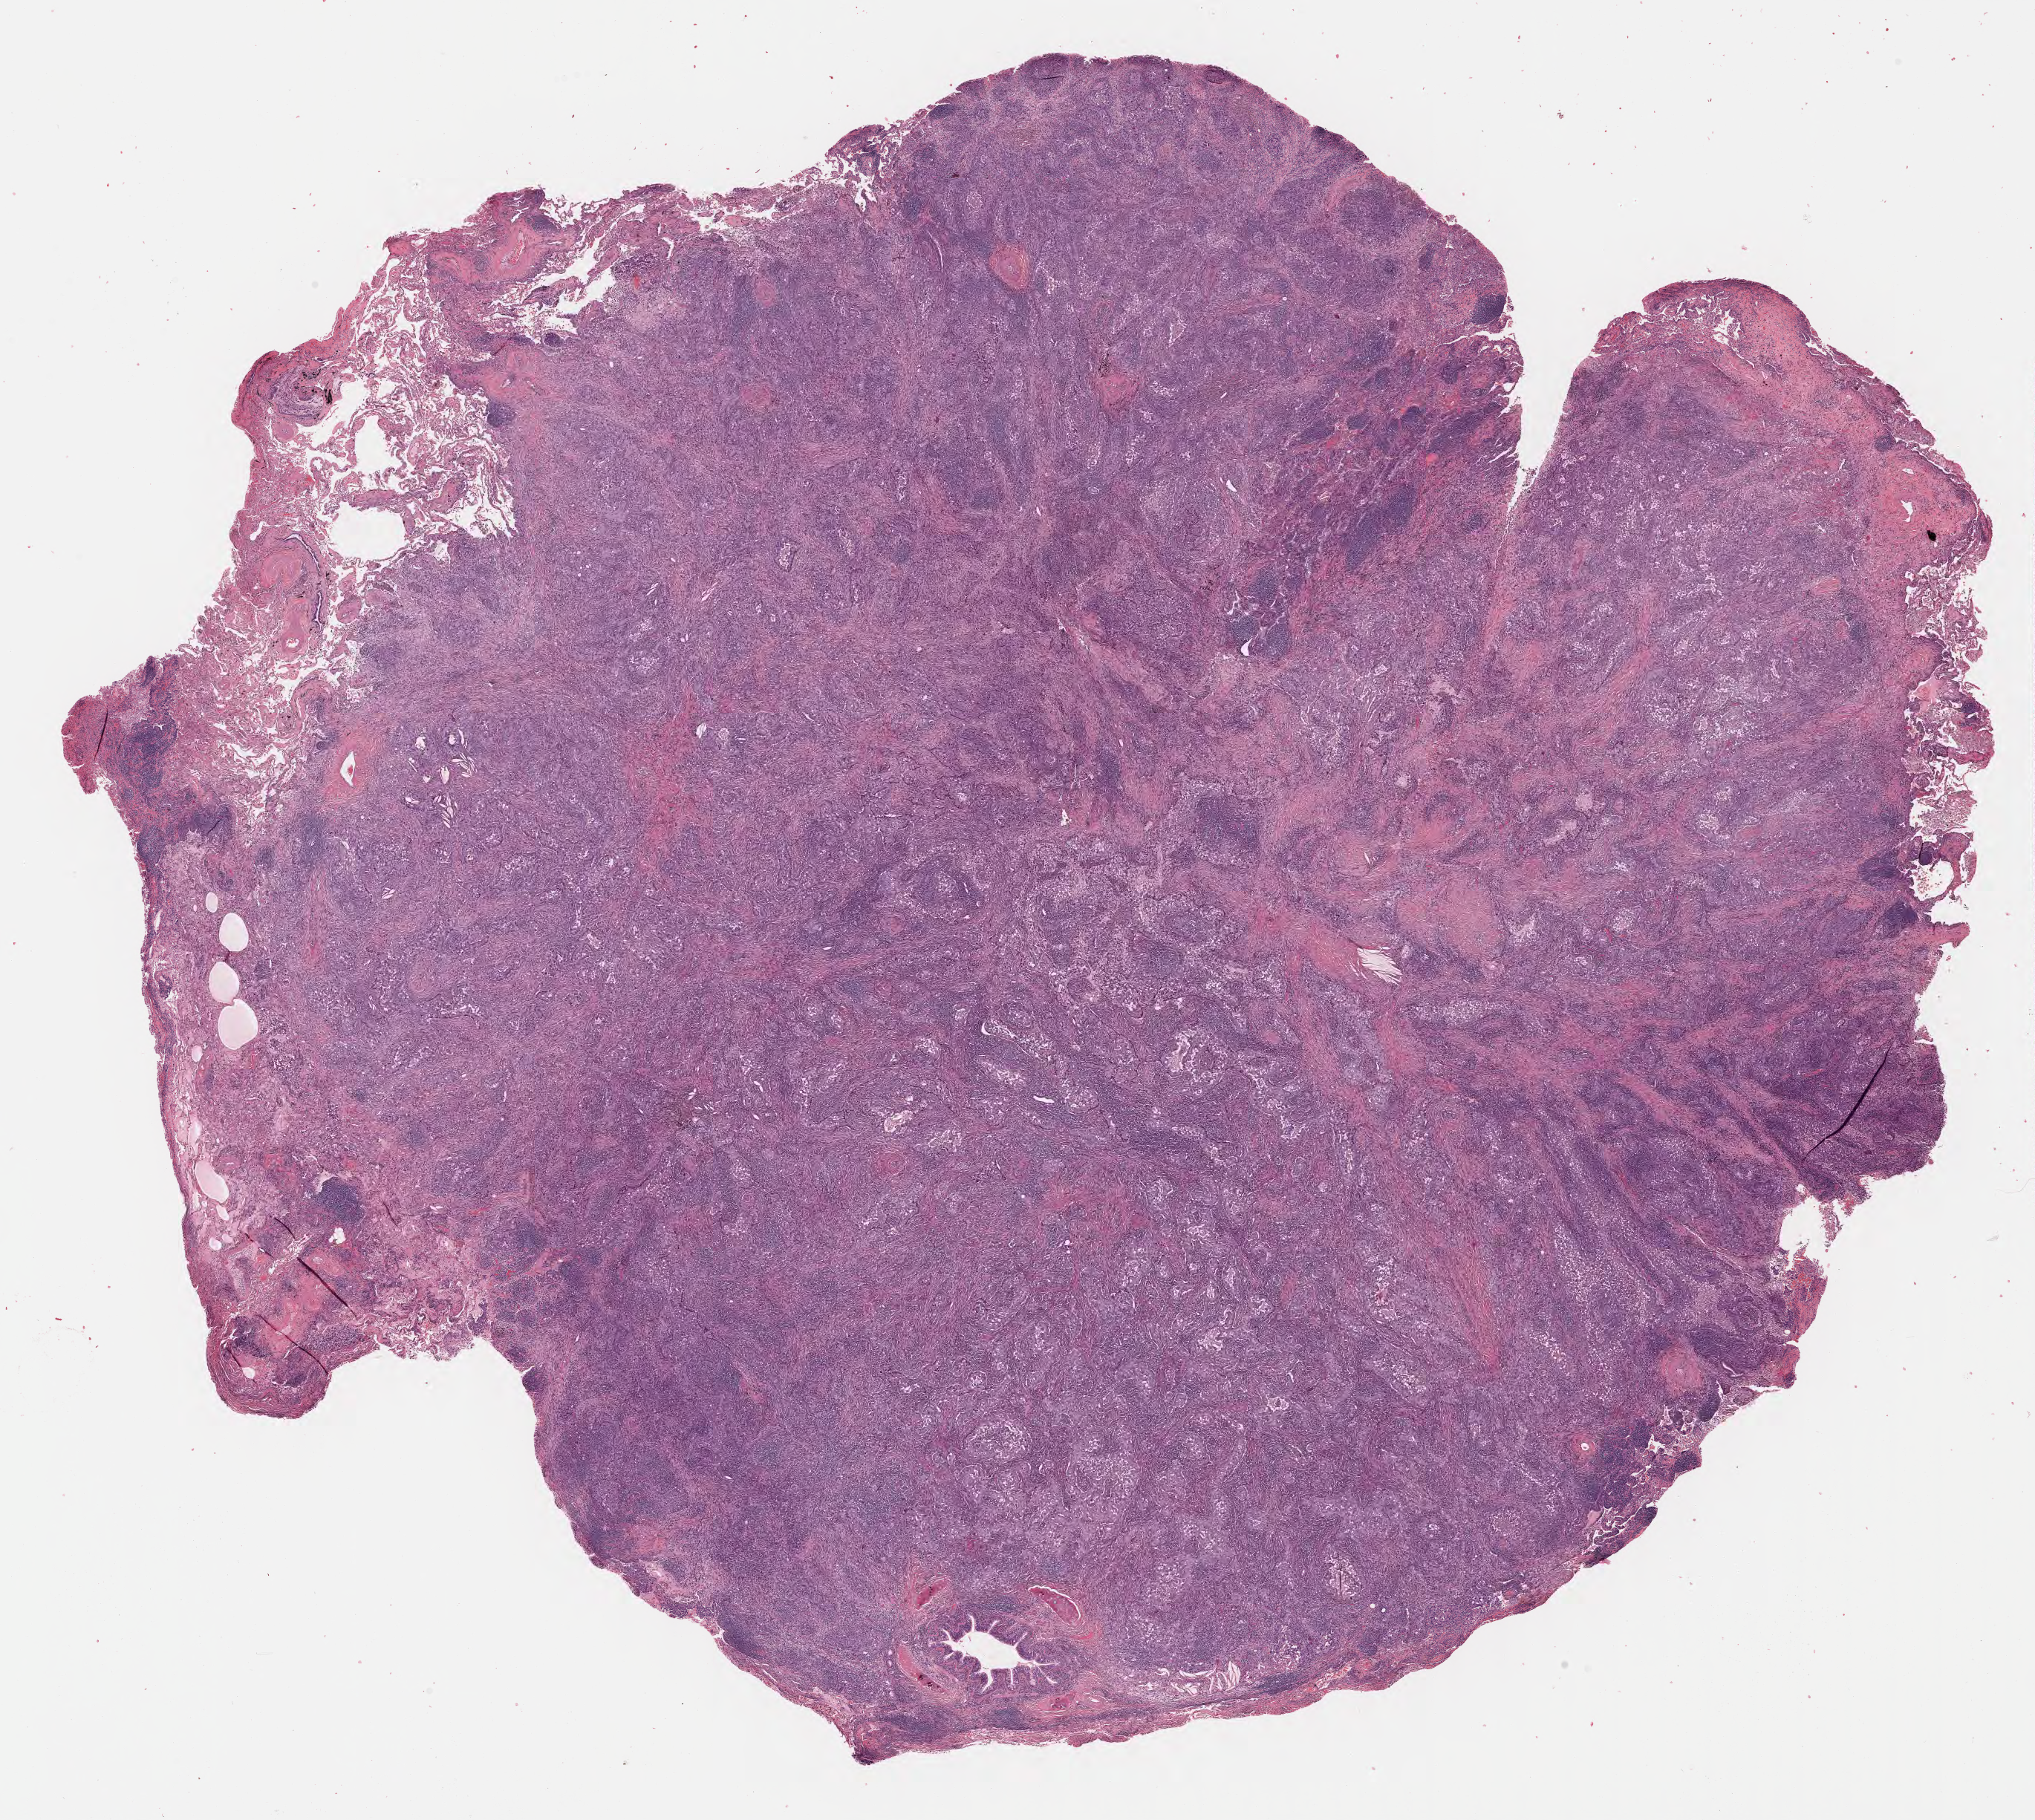
Whole-slide histology image, H&E — whole scanned area (about 22.1 x 19.8 mm, acquisition: 40x scan) shown as a low-resolution overview; formalin-fixed paraffin-embedded (FFPE) diagnostic section; sample: primary tumour, lung. Female, age 62 years at initial diagnosis.
Pathologic diagnosis: Signet ring cell carcinoma (upper lobe, lung).